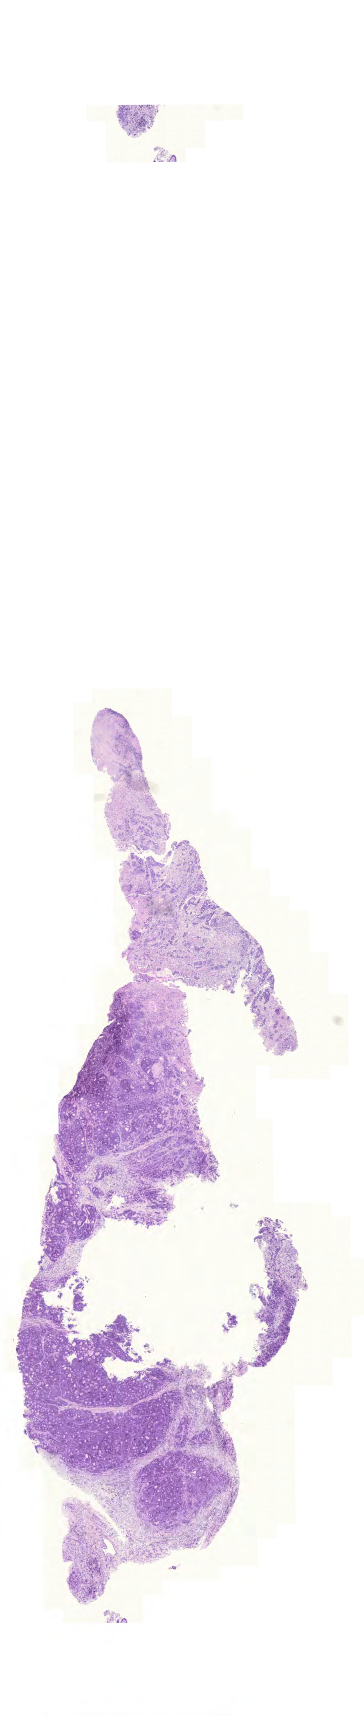
Whole-slide histology image, H&E-stained — low-resolution overview of the scanned area, about 5.4 x 25.5 mm (from a 20x scan), FFPE section, sample: primary tumour, colon. Patient: female, age at initial diagnosis 71 years.
TNM: T3 N2 M1. Pathologic diagnosis: Adenocarcinoma, NOS (ascending colon). AJCC pathologic stage: IV (6th edition).